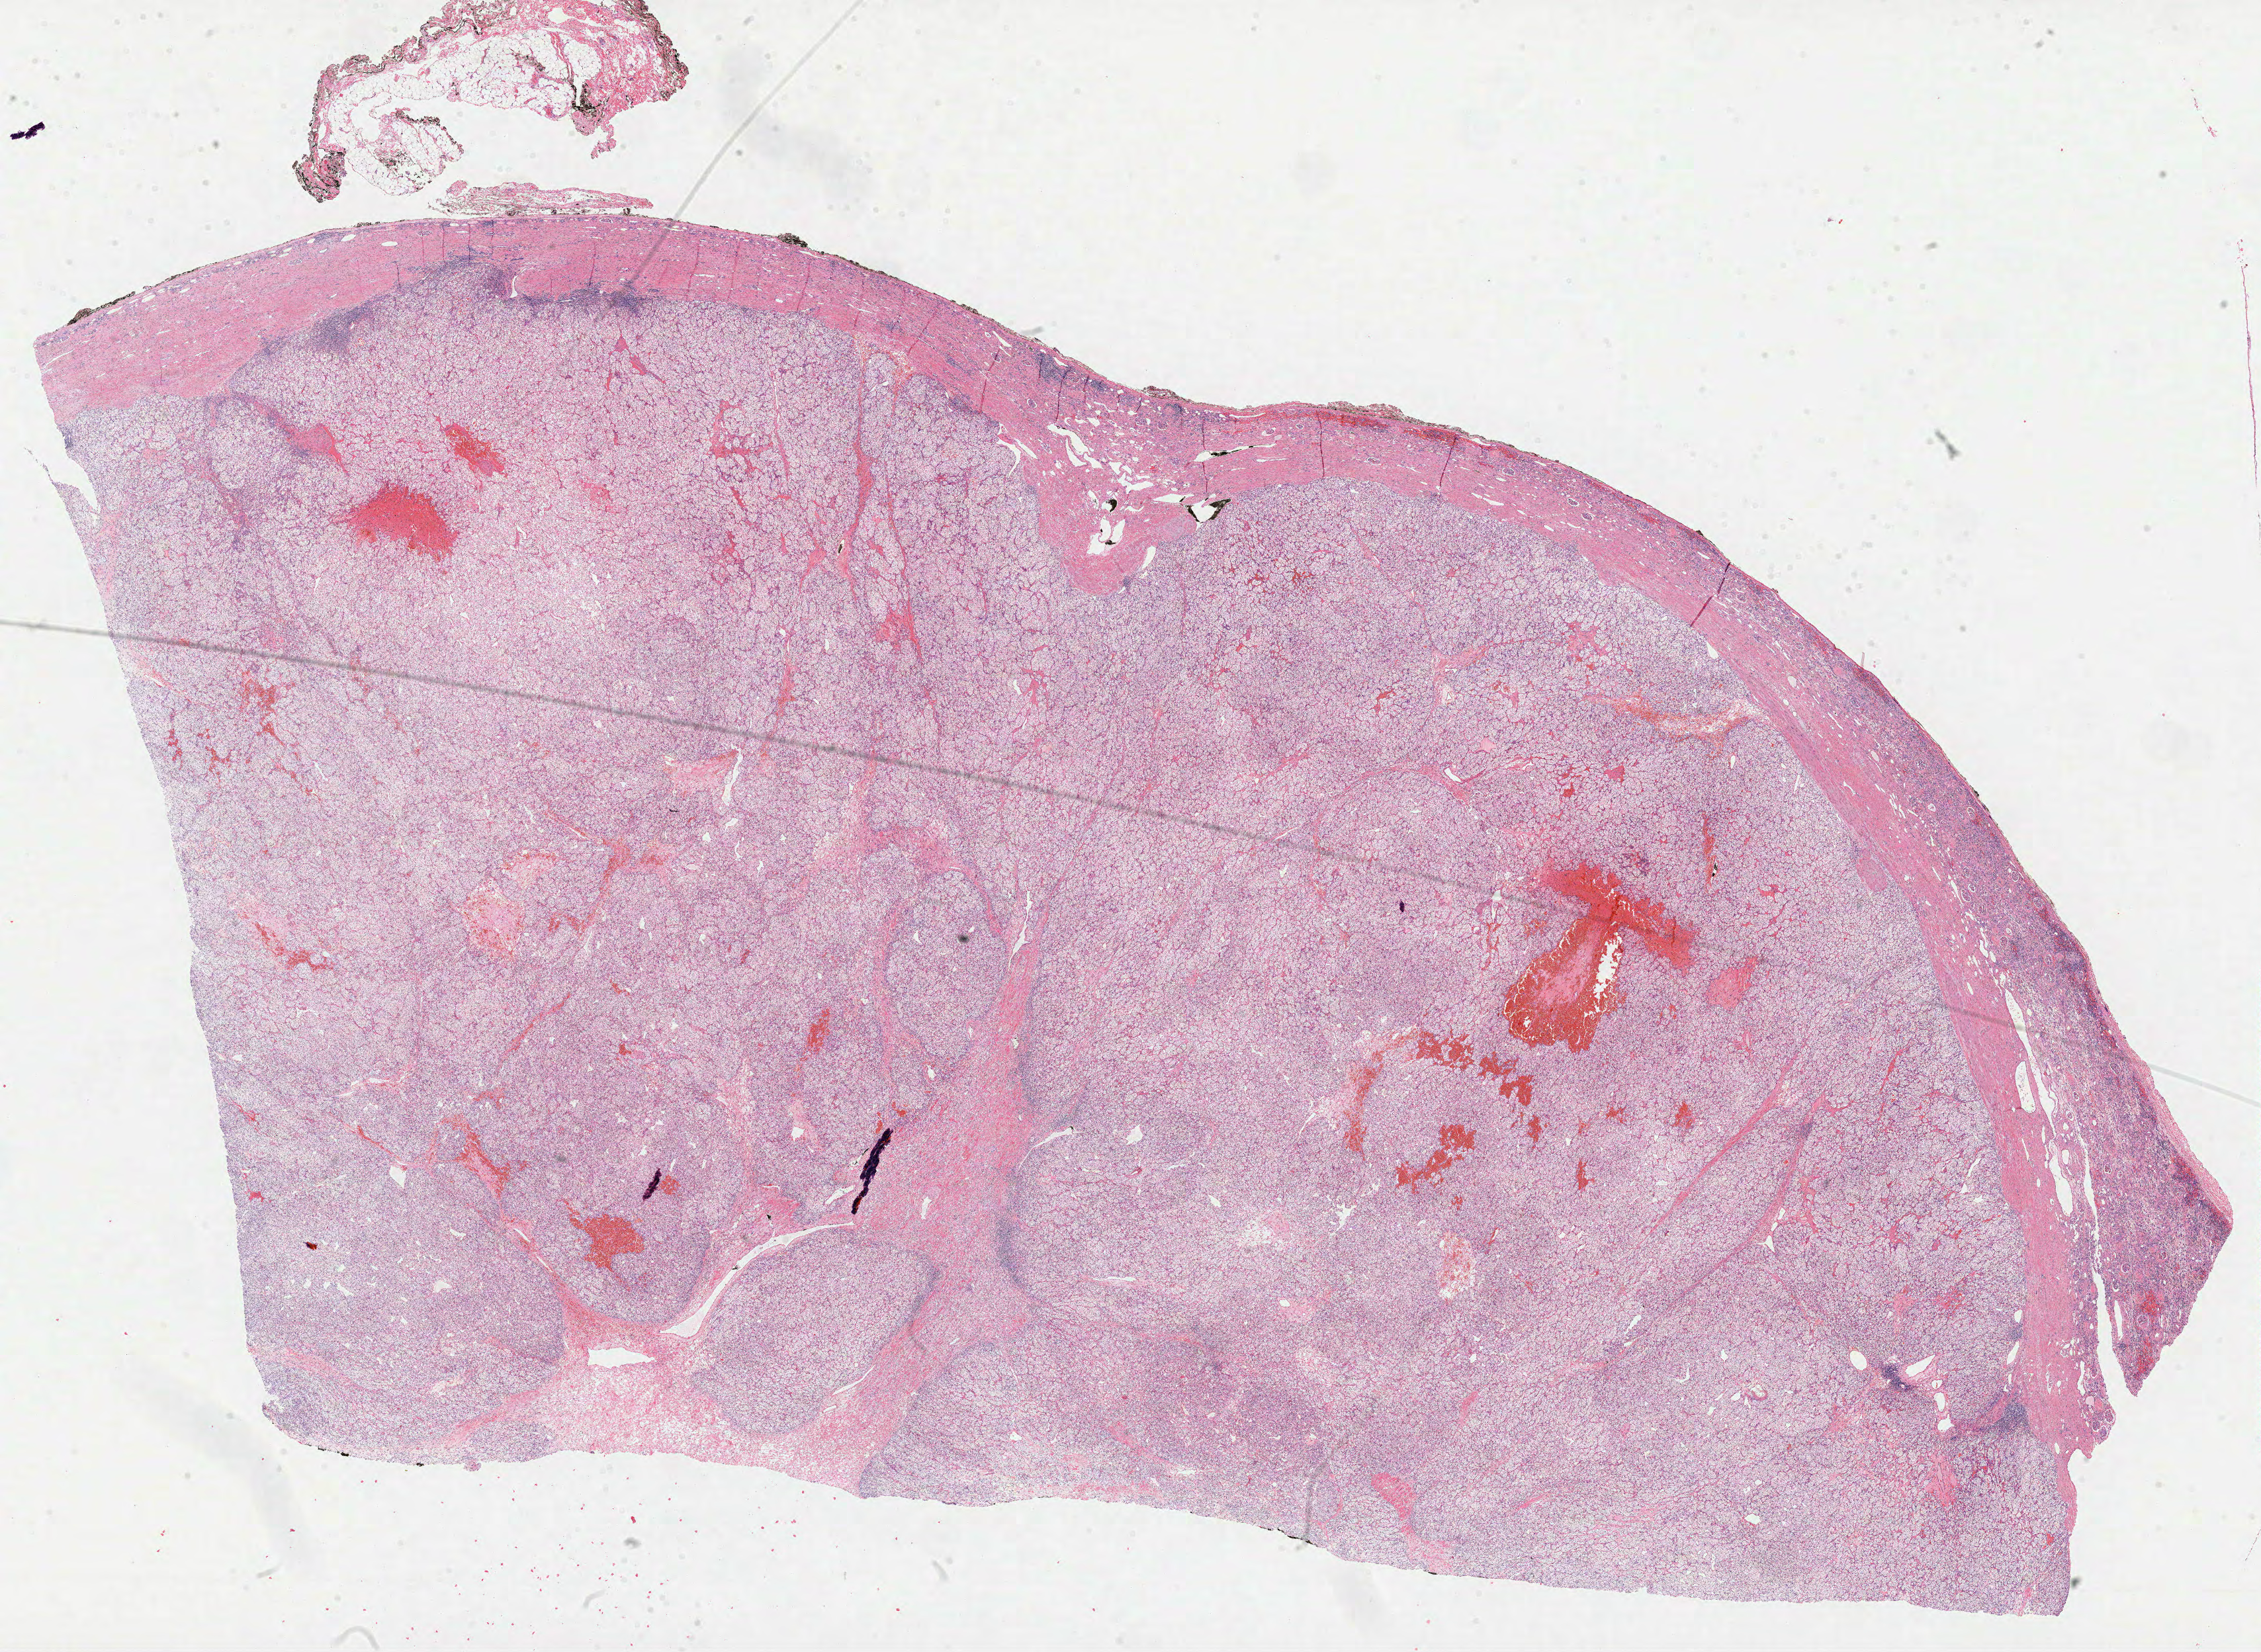
Digitized H&E tissue section (whole slide), shown as a low-resolution overview of the whole scanned area (about 27.6 x 20.1 mm), formalin-fixed paraffin-embedded (FFPE) diagnostic section, kidney, primary tumour sample. Female patient; age at initial diagnosis 47 years. Histologic grade: G1 (well differentiated).
• AJCC pathologic stage: I (6th edition)
• pathologic diagnosis: Clear cell adenocarcinoma, NOS
• laterality: right
• TNM: T1 NX M0